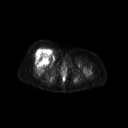
FDG PET of an extremity soft-tissue mass (from a PET/CT study), one axial slice; slice 57 of 267 in the series (ordered by position); 3.27 mm slice thickness; 128 × 128 image matrix, field of view 700 × 700 mm. Female patient, age 56 years. Case-level facts recorded for this patient, not image findings: histological type: malignant solitary fibrous tumor; grade: intermediate; site of the primary tumour: right thigh.
Outlined on this slice (expert contour drawn on MRI and transferred to this co-registered scan by the dataset authors):
- gross tumour volume including surrounding oedema: bounding box (x1, y1, x2, y2) in pixels: (34, 48, 53, 62)
- gross tumour volume (mass): (34, 48, 52, 62)